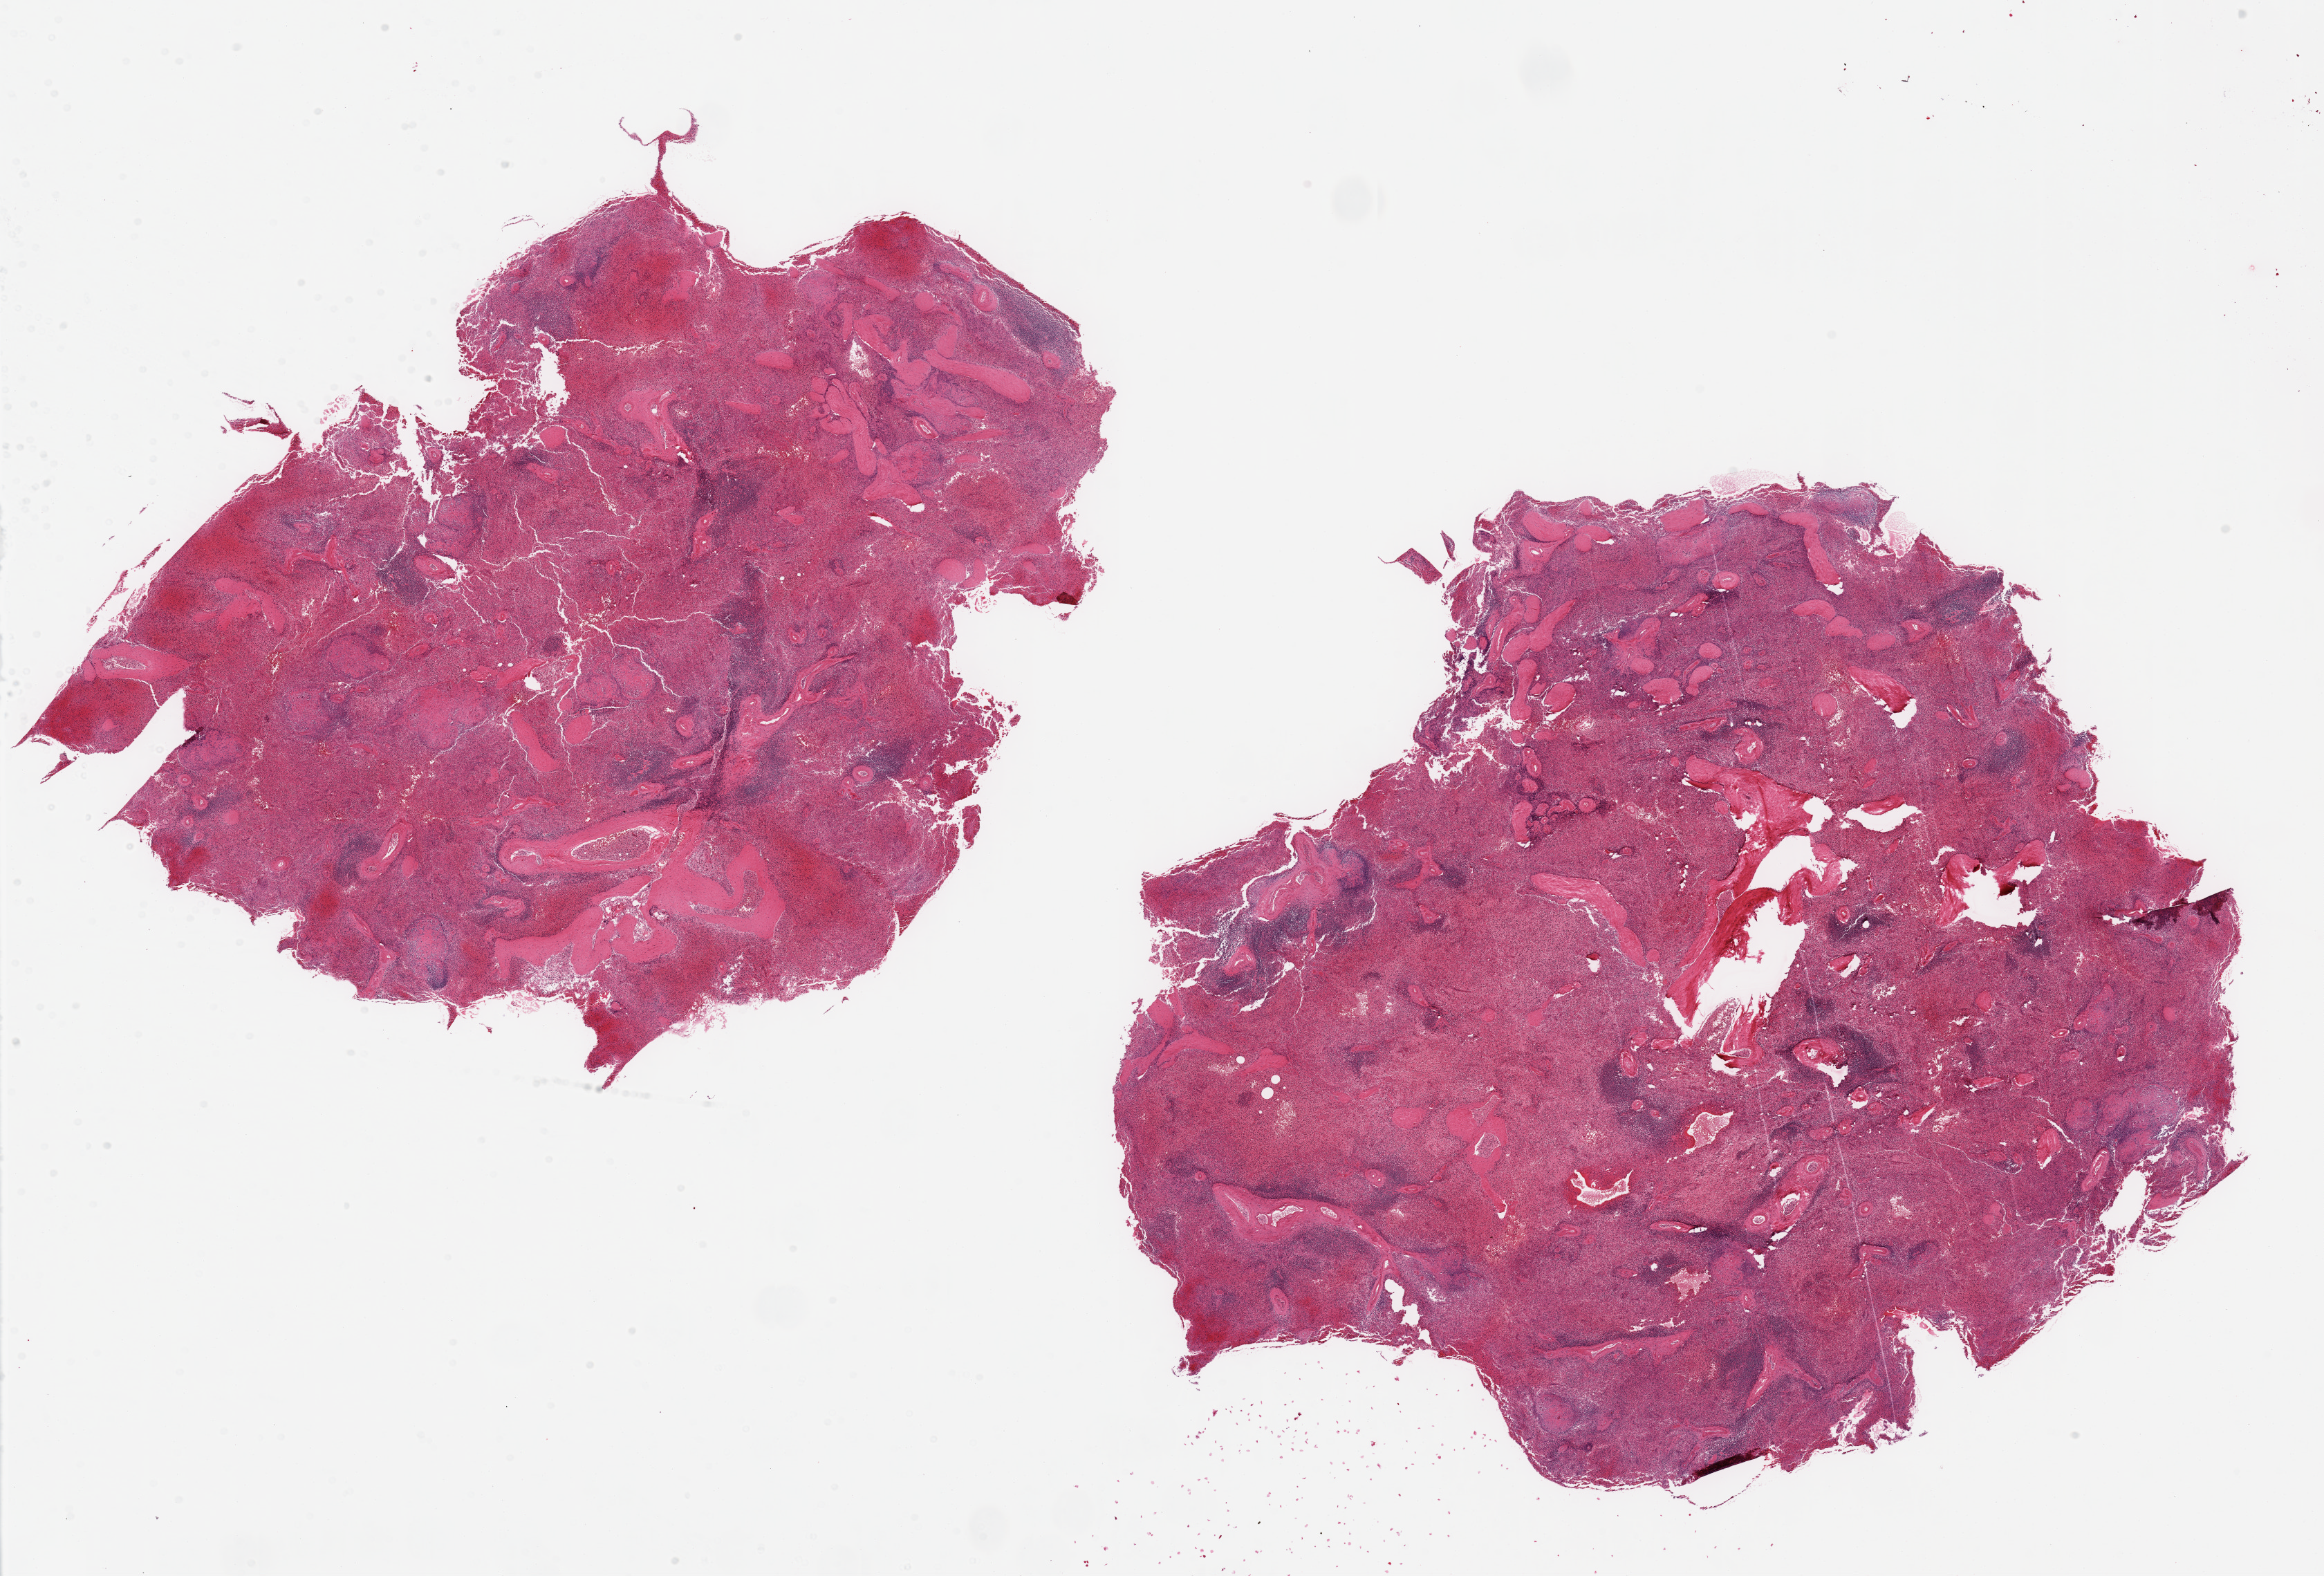
H&E whole-slide image — a low-resolution overview of the entire scanned area, about 26.6 x 18.0 mm, PAXgene-fixed paraffin-embedded (PFPE) section, sampled site (target tissue): spleen, donor tissue sample. Male donor.
Reviewer comment on this tissue sample: 2 pieces, moderate congestion.